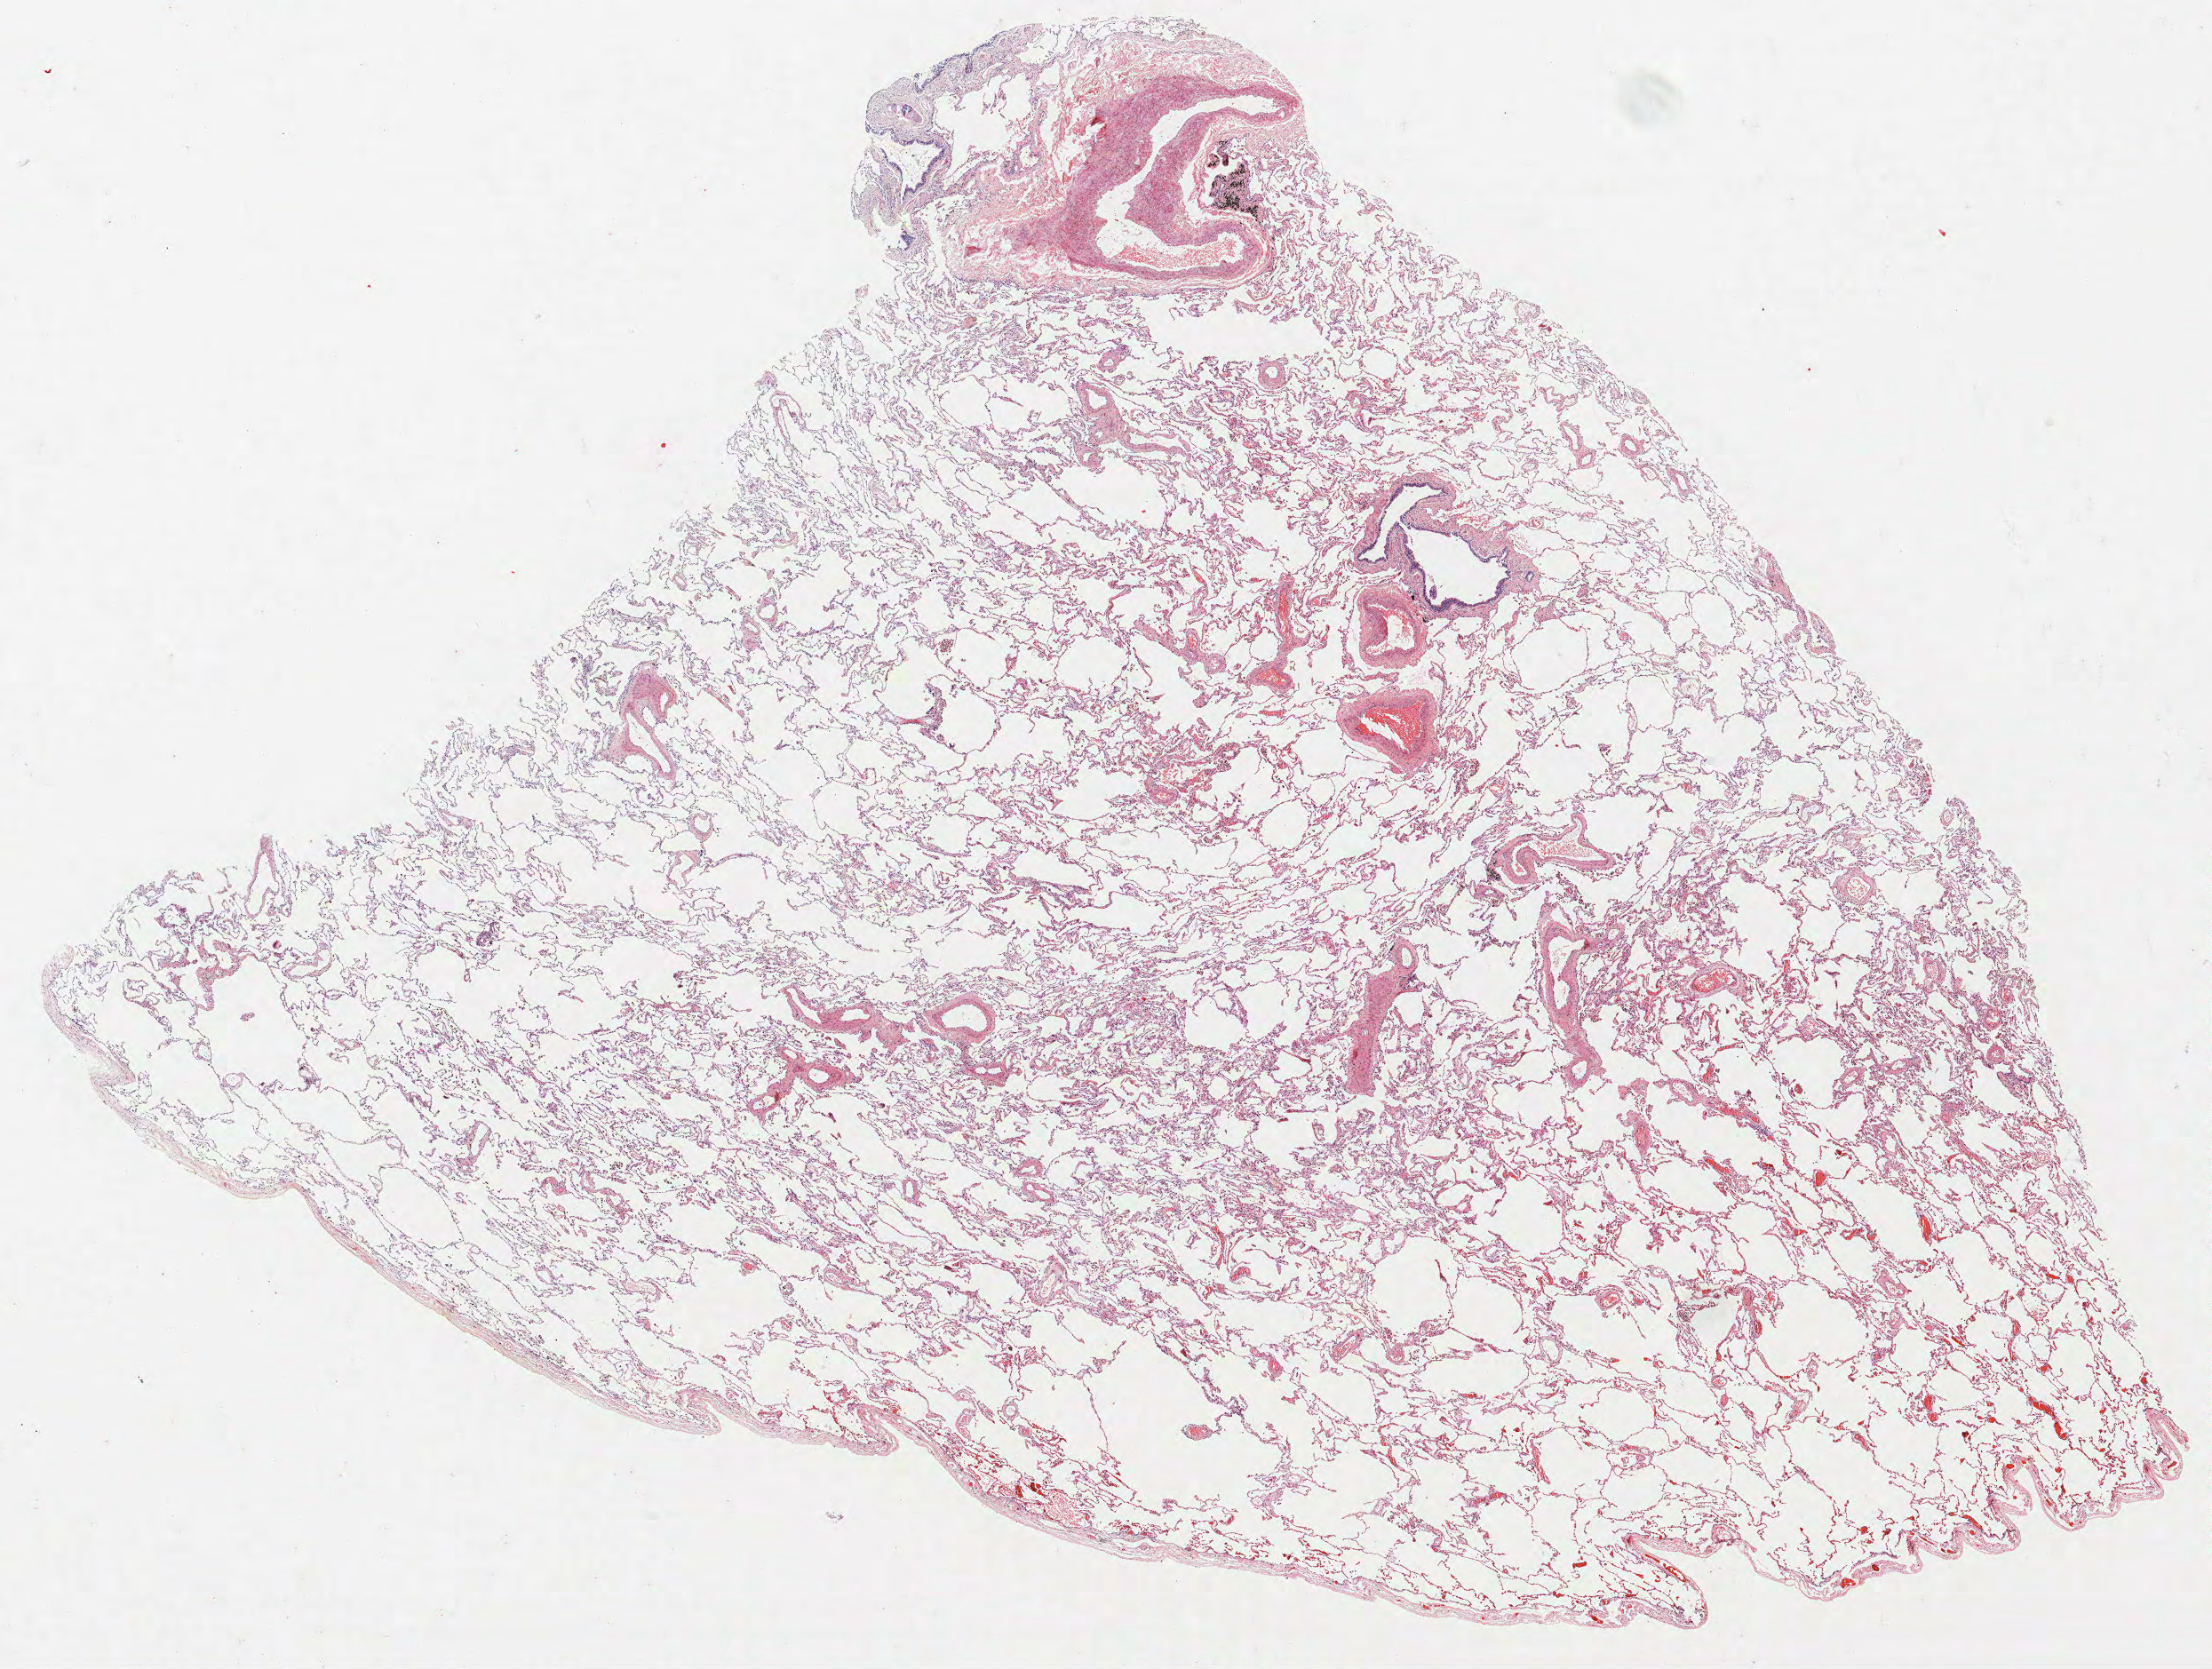
H&E-stained whole-slide image, a low-resolution overview of the entire scanned area, about 19.9 x 15.0 mm; FFPE section; lung tissue. Male patient, aged 74 at enrolment.
Participant's lung-cancer diagnosis: Bronchiolo-alveolar adenocarcinoma, NOS.